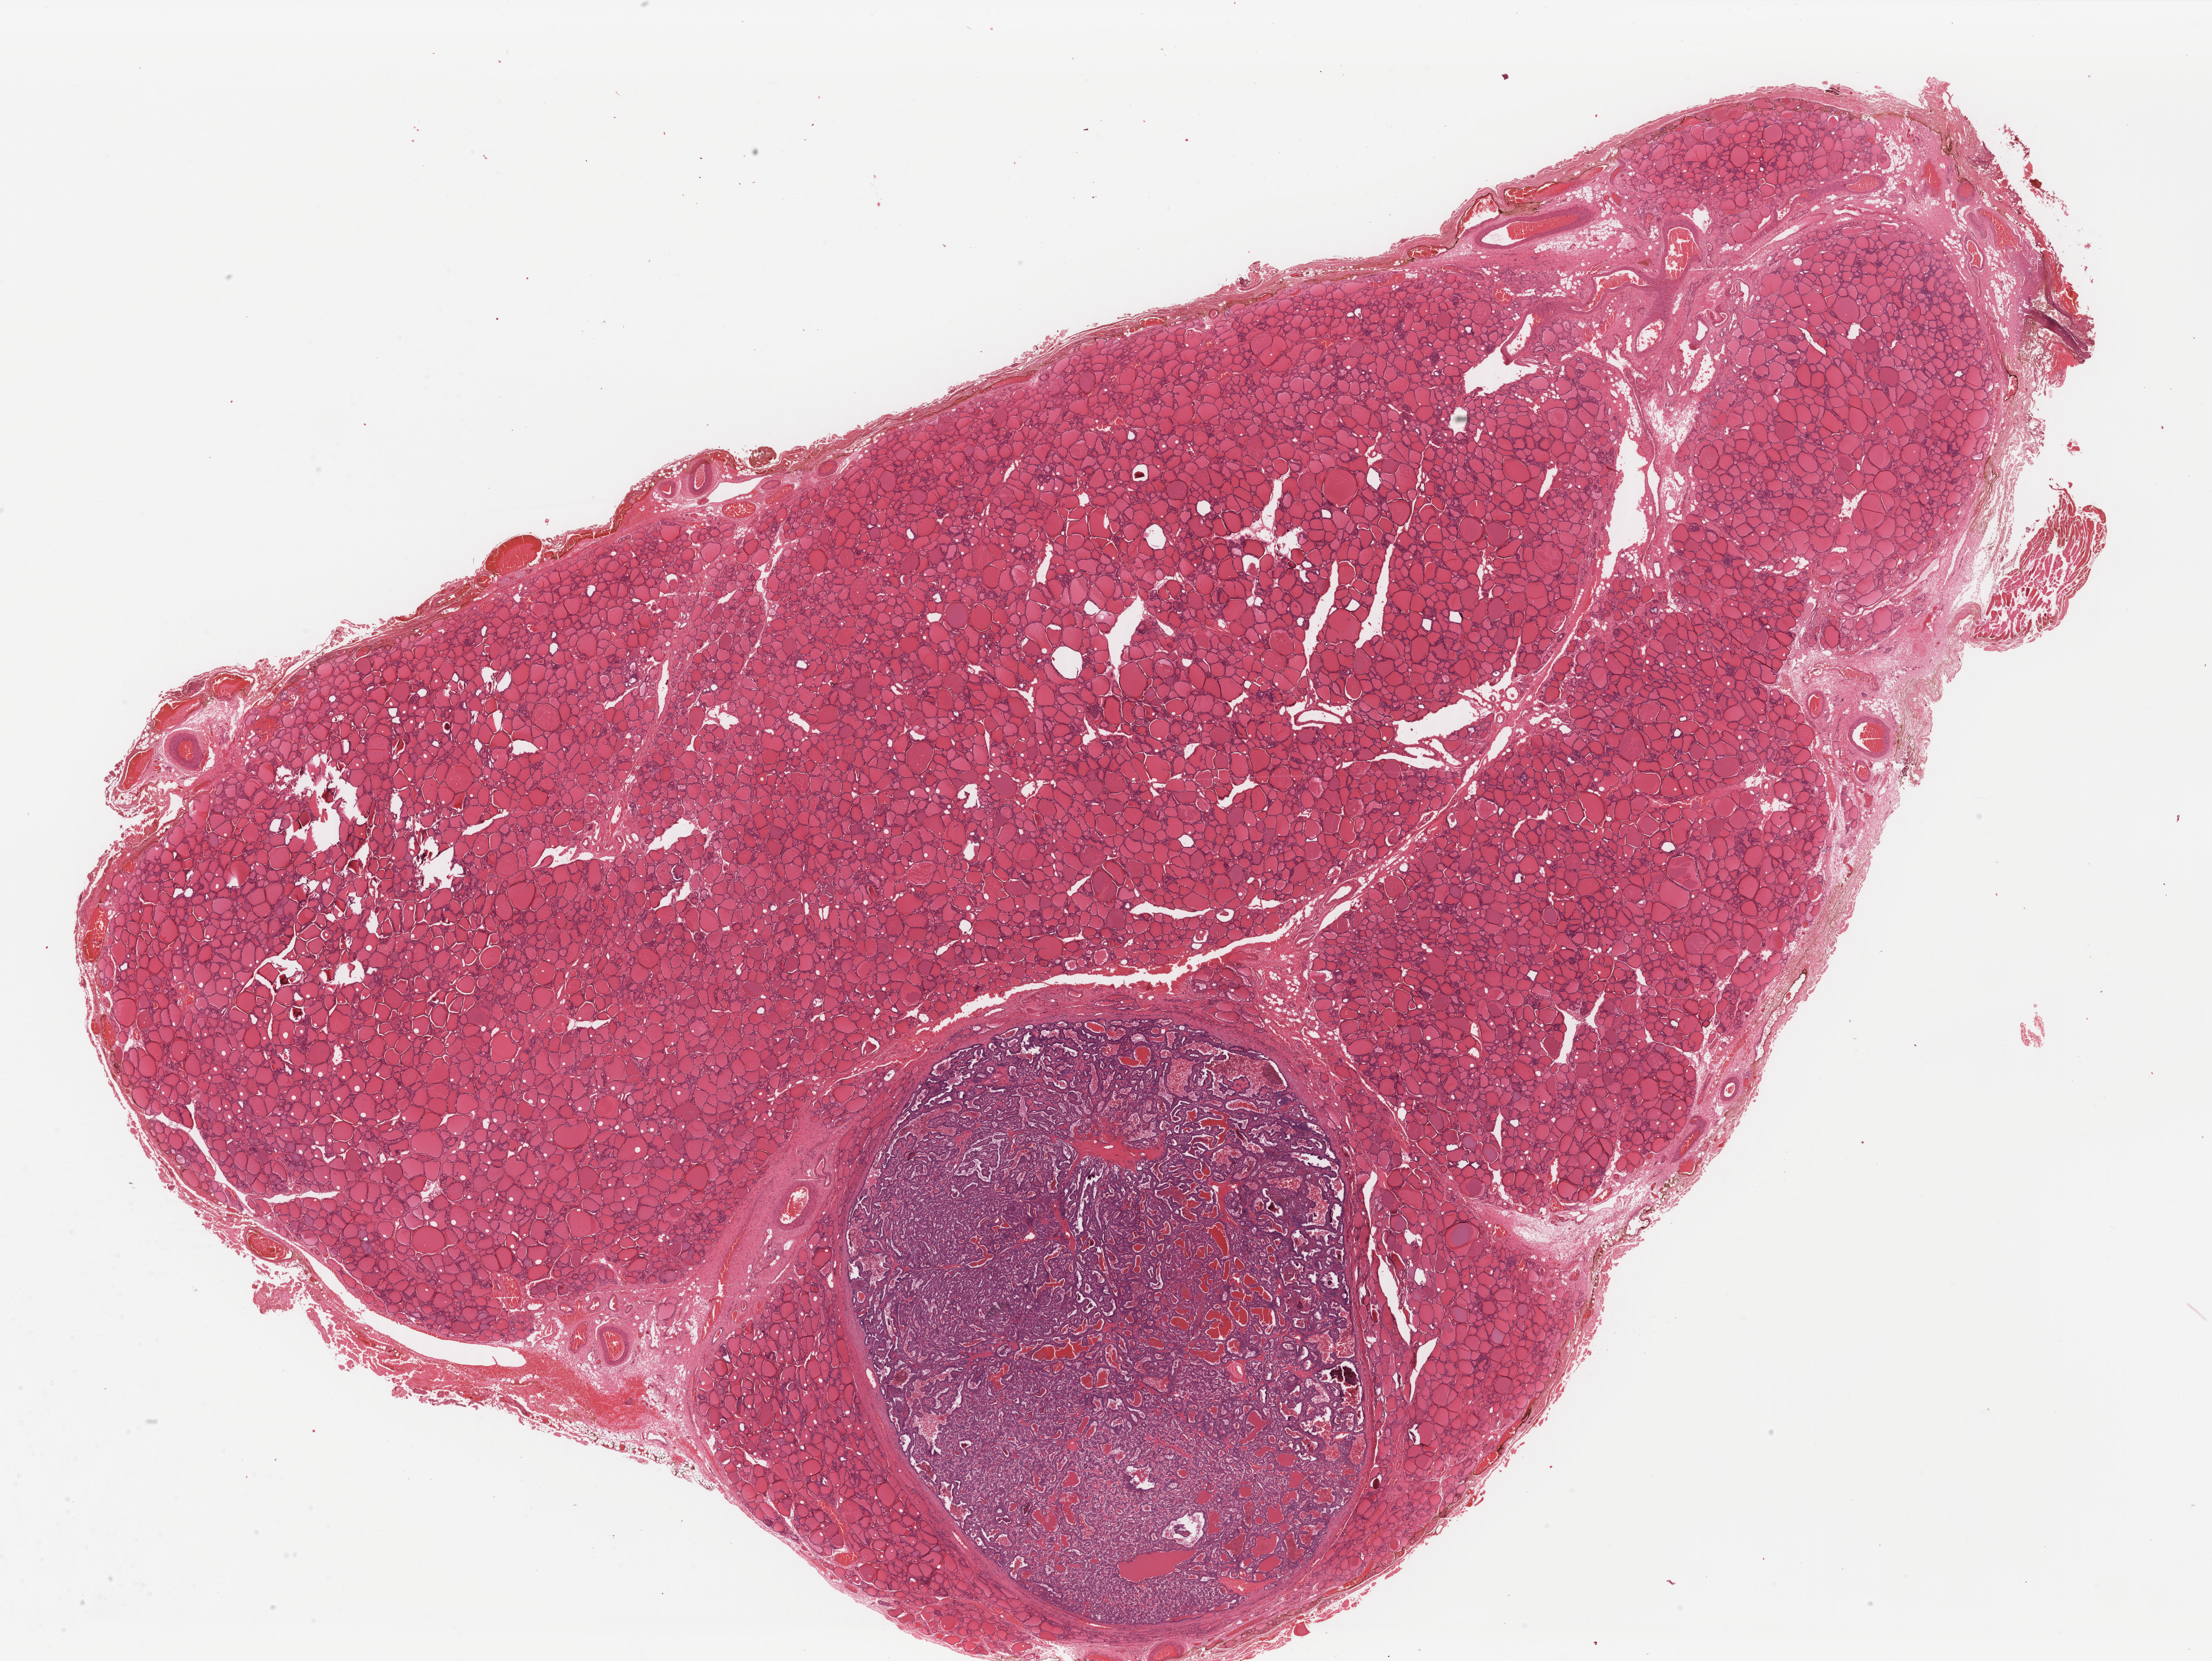
Hematoxylin and eosin (H&E) stained whole-slide image — low-resolution overview of the scanned area, about 29.7 x 22.3 mm (slide scanned at 40x); formalin-fixed paraffin-embedded (FFPE) diagnostic section; primary tumour sample from the thyroid. Female patient; age at initial diagnosis 32 years.
* histologic diagnosis: Papillary adenocarcinoma, NOS
* AJCC pathologic stage: I
* laterality: left